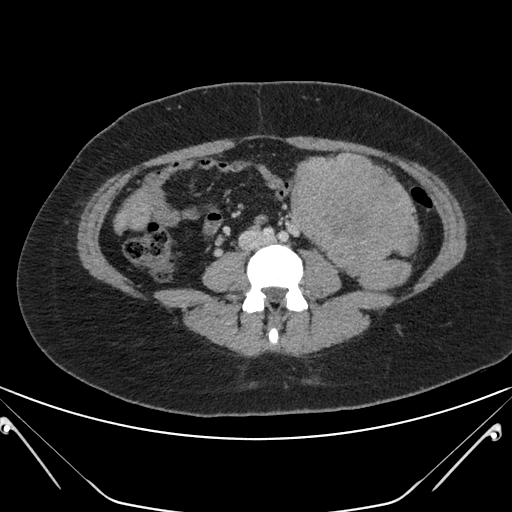
Contrast-enhanced abdominal CT, one axial slice. Position 82 of 168 along the scan axis. 120 kVp. Soft-tissue window (W 400 / L 40 HU). 512 × 512 image matrix, field of view 394 × 394 mm. Female patient, age 26 years. From the clinical record (not read from this slice): diagnosis: adrenocortical carcinoma; tumour side: left adrenal.
Outlined on this slice (semi-automatically segmented with operator editing):
- mass: bounding box <291,152,418,289> (left, top, right, bottom; pixels)